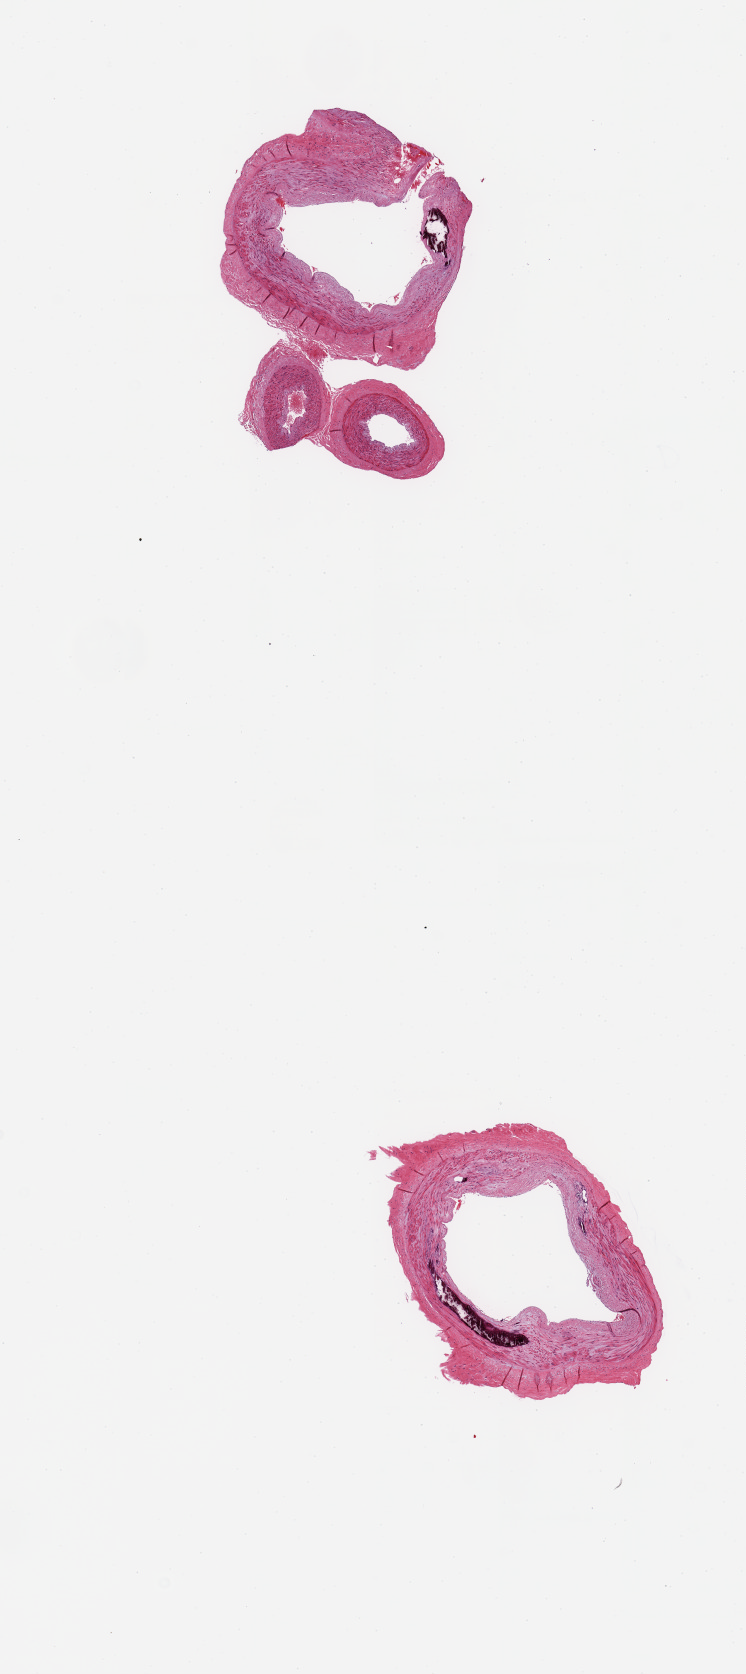
H&E whole-slide image, brightfield, whole scanned area (about 5.9 x 13.3 mm, from a 20x scan) shown as a low-resolution overview; PAXgene-fixed, paraffin-embedded tissue; sampled site (target tissue): tibial artery; tissue donor sample. Donor: female.
* reviewer comment on this tissue sample: 2 pieces; medial calcifications; atherosis; lumina patent